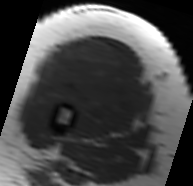
MRI of an extremity soft-tissue mass, one axial slice; position 32 of 91 along the scan axis; MR volume resampled by the dataset authors to the PET/CT grid (not the native acquisition matrix); 3.27 mm slice thickness; 193 × 186 image matrix. Female patient. From the clinical record (not read from this slice): histological type: malignant solitary fibrous tumor; grade: intermediate; site of the primary tumour: right thigh.
Outlined on this slice (expert contour drawn on MRI and transferred to this co-registered scan by the dataset authors):
- gross tumour volume including surrounding oedema: box from (x=37, y=39) to (x=150, y=129) px
- gross tumour volume (mass): (x=42, y=39)–(x=146, y=125)